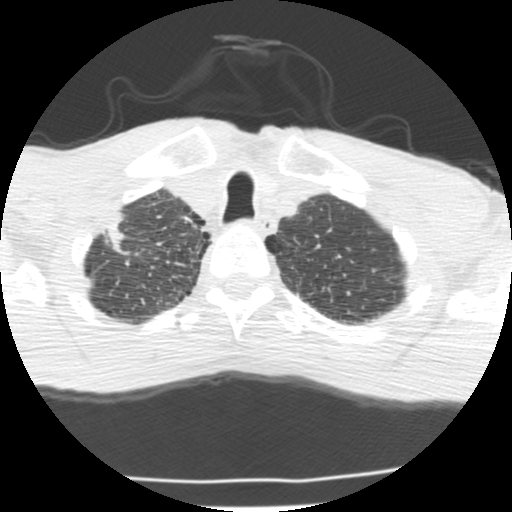
Axial slice from a low-dose chest CT screening exam. Second screening round (one year after baseline). Lung window (W 1500 / L -600 HU). 2.5 mm slice thickness. 512 × 512 image matrix, field of view 283 × 283 mm. Male, age 62 years at enrolment. Current smoker at enrolment.
Expert-annotated lung lesion, box from (x=76, y=212) to (x=142, y=273) px. The exam's reader record, not a measurement of the box and not confirmed to be the same lesion: non-calcified nodule or mass ≥4 mm, right upper lobe, 23 × 11 mm, spiculated (stellate) margins, soft tissue attenuation, pre-existing on the prior screen: yes. Later outcome: lung cancer diagnosed 277 days after this screen — adenocarcinoma, NOS, right upper lobe, poorly differentiated (G3), stage IIA (AJCC 6th edition), 22 mm at pathology.